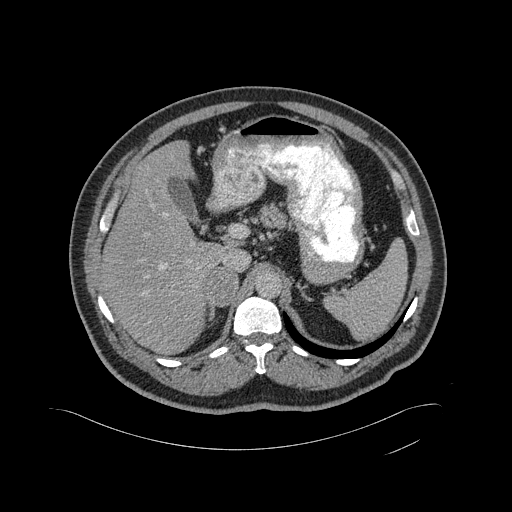
Contrast-enhanced abdominal CT, one axial slice. Position 326 of 433 along the scan axis. 120 kVp. Intravenous contrast given. Soft-tissue window (W 400 / L 40 HU). 2 mm slice thickness. 512 × 512 image matrix, field of view 500 × 500 mm. Male patient, age 56 years. From the clinical record (not read from this slice): diagnosis: adrenocortical carcinoma; tumour side: right adrenal.
Structures marked on this image (semi-automatically segmented with operator editing):
- mass: bounding box [x1, y1, x2, y2] px = [206, 268, 237, 304]